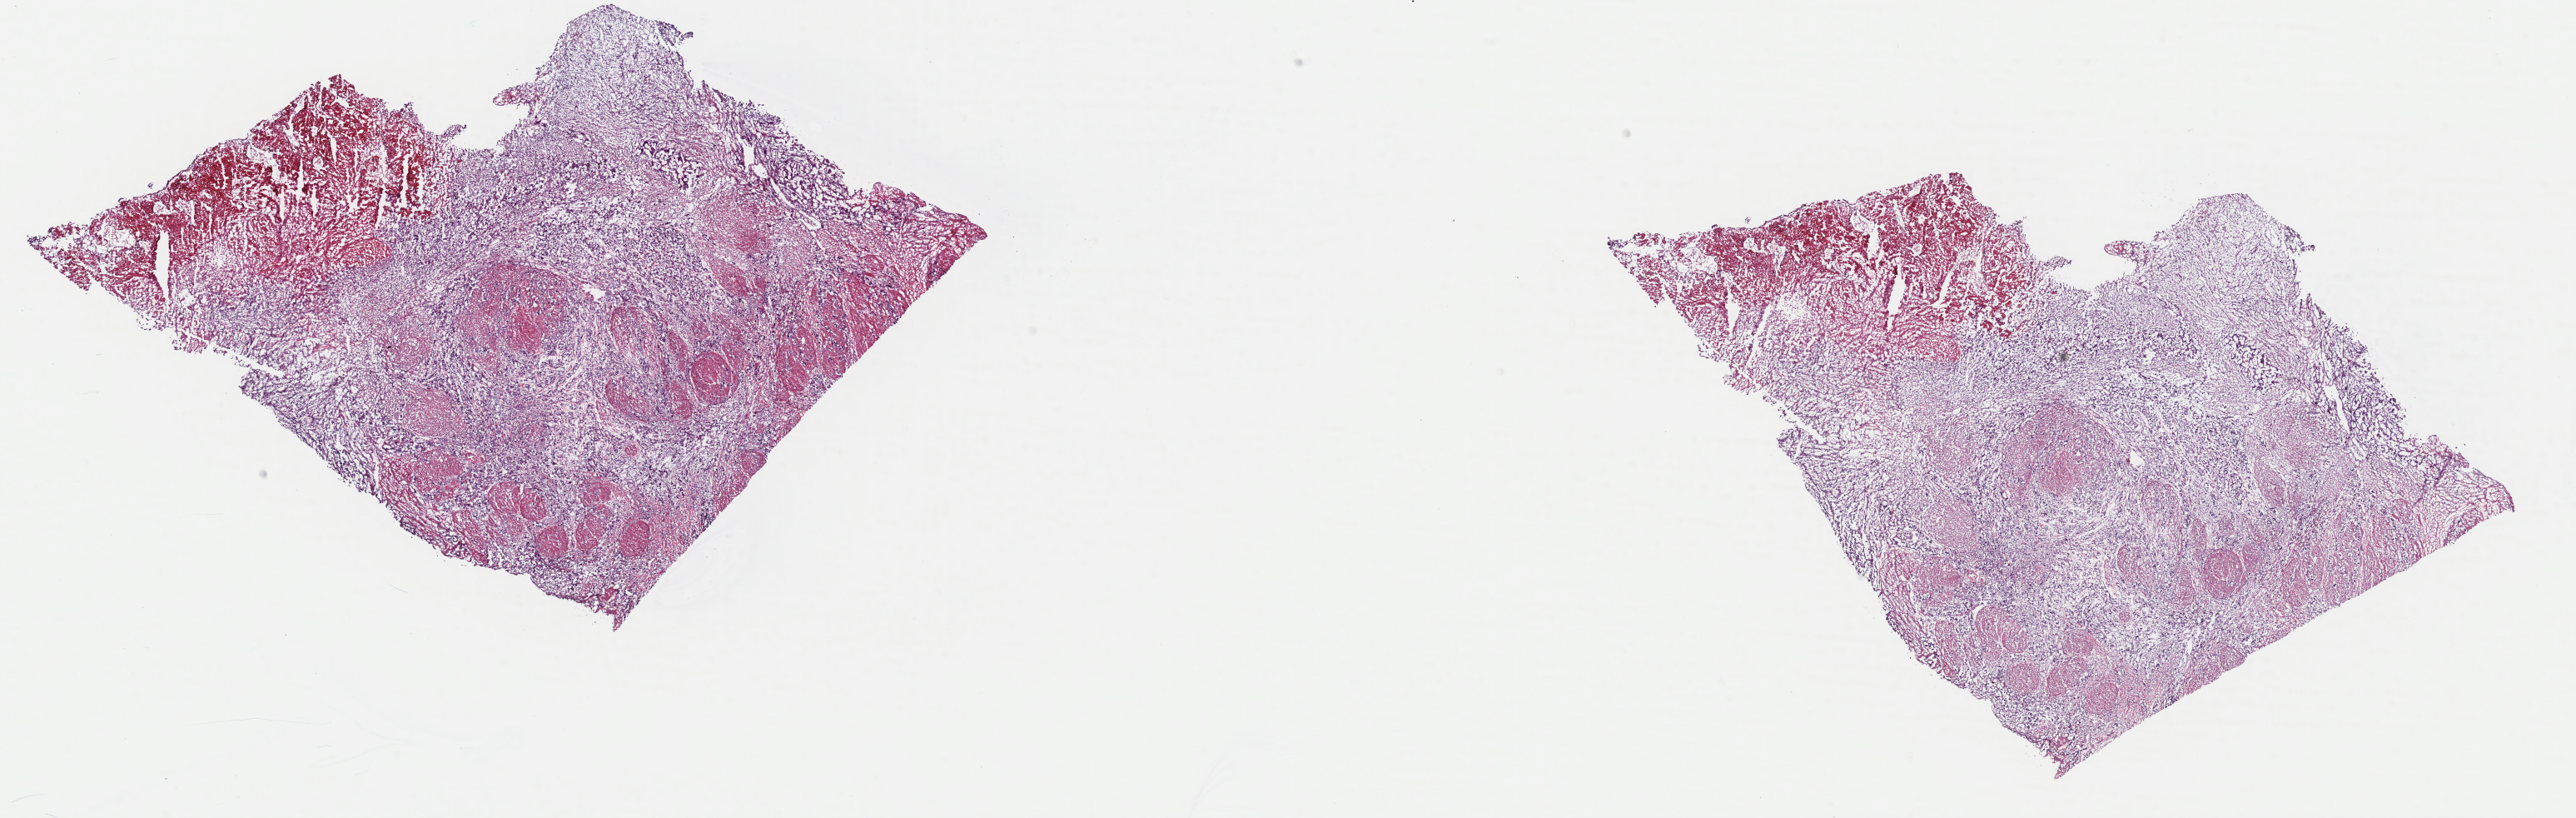
Digitized Hematoxylin and eosin (H&E) stained tissue section (whole slide), low-resolution overview of the scanned area, about 24.4 x 7.8 mm; frozen section from the top of the tissue portion; primary tumour sample from the bladder. Male patient; age at initial diagnosis 62 years. Slide review estimates, as recorded: tumour cells 75%, tumour nuclei 80%.
Diagnosis: Transitional cell carcinoma (lateral wall of bladder).